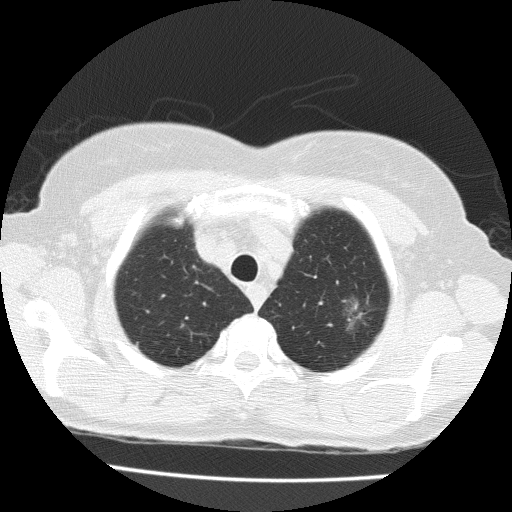
Low-dose screening chest CT, axial slice. Baseline annual screen. Lung window (W 1500 / L -600 HU). 2 mm slice thickness. Lung (sharp) reconstruction kernel (FC51). Slice 28 of 183 in the series. 512 × 512 image matrix, field of view 320 × 320 mm. Female participant, aged 71 years at enrolment. Former smoker at enrolment.
Expert-annotated lung lesion, bounding box [x1, y1, x2, y2] px = [336, 290, 390, 339]. Screening reader's record for this exam (one nodule recorded; not confirmed to be the boxed lesion): non-calcified nodule or mass ≥4 mm, left upper lobe, 15 × 10 mm, spiculated (stellate) margins, soft tissue attenuation. Official screen result: positive, change unspecified: nodule(s) >= 4 mm or enlarging nodule(s), mass(es), or other non-specific abnormalities suspicious for lung cancer.